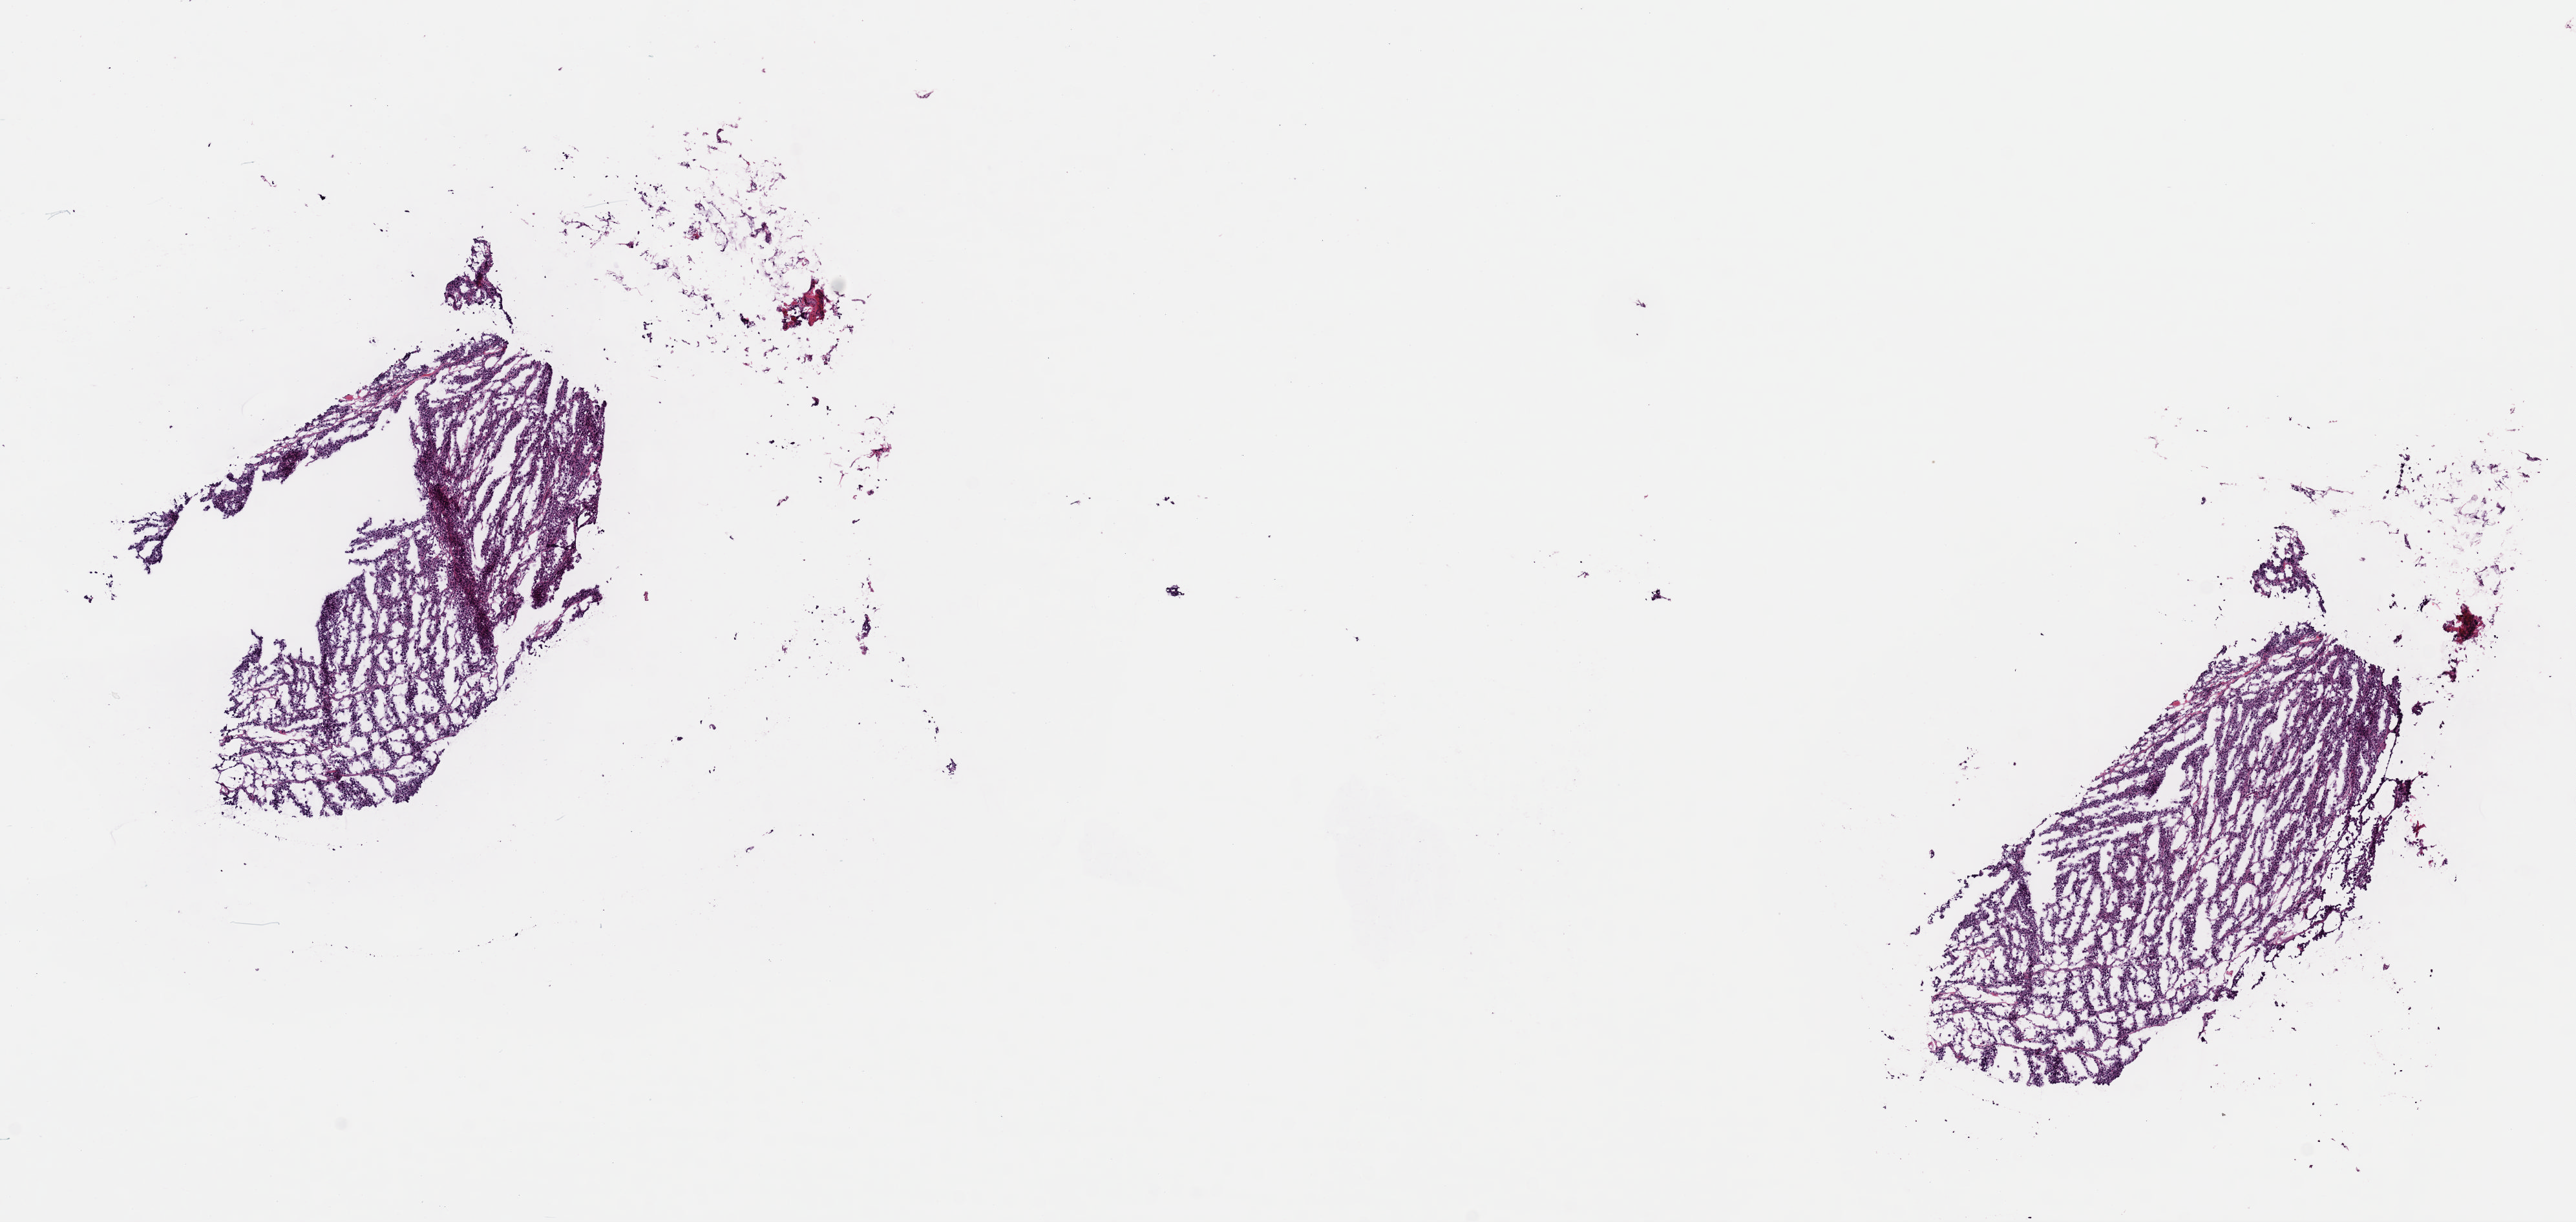
Digitized Hematoxylin and eosin (H&E) stained tissue section (whole slide), low-resolution overview of the scanned area, about 15.7 x 7.5 mm (slide scanned at 40x); frozen section from the top of the tissue portion; metastatic tumour sample, sampled site not recorded. Patient: male, age at initial diagnosis 38 years. Pathologist review of this section (percent, as recorded): tumour cells 90%, tumour nuclei 90%, normal cells 0%, stromal cells 10%, necrosis 0%. Infiltration values recorded for this section: lymphocyte infiltration 2%, monocyte infiltration 1%, neutrophil infiltration 1%.
* this section: metastatic tumour tissue
* patient diagnosis: Malignant melanoma, NOS